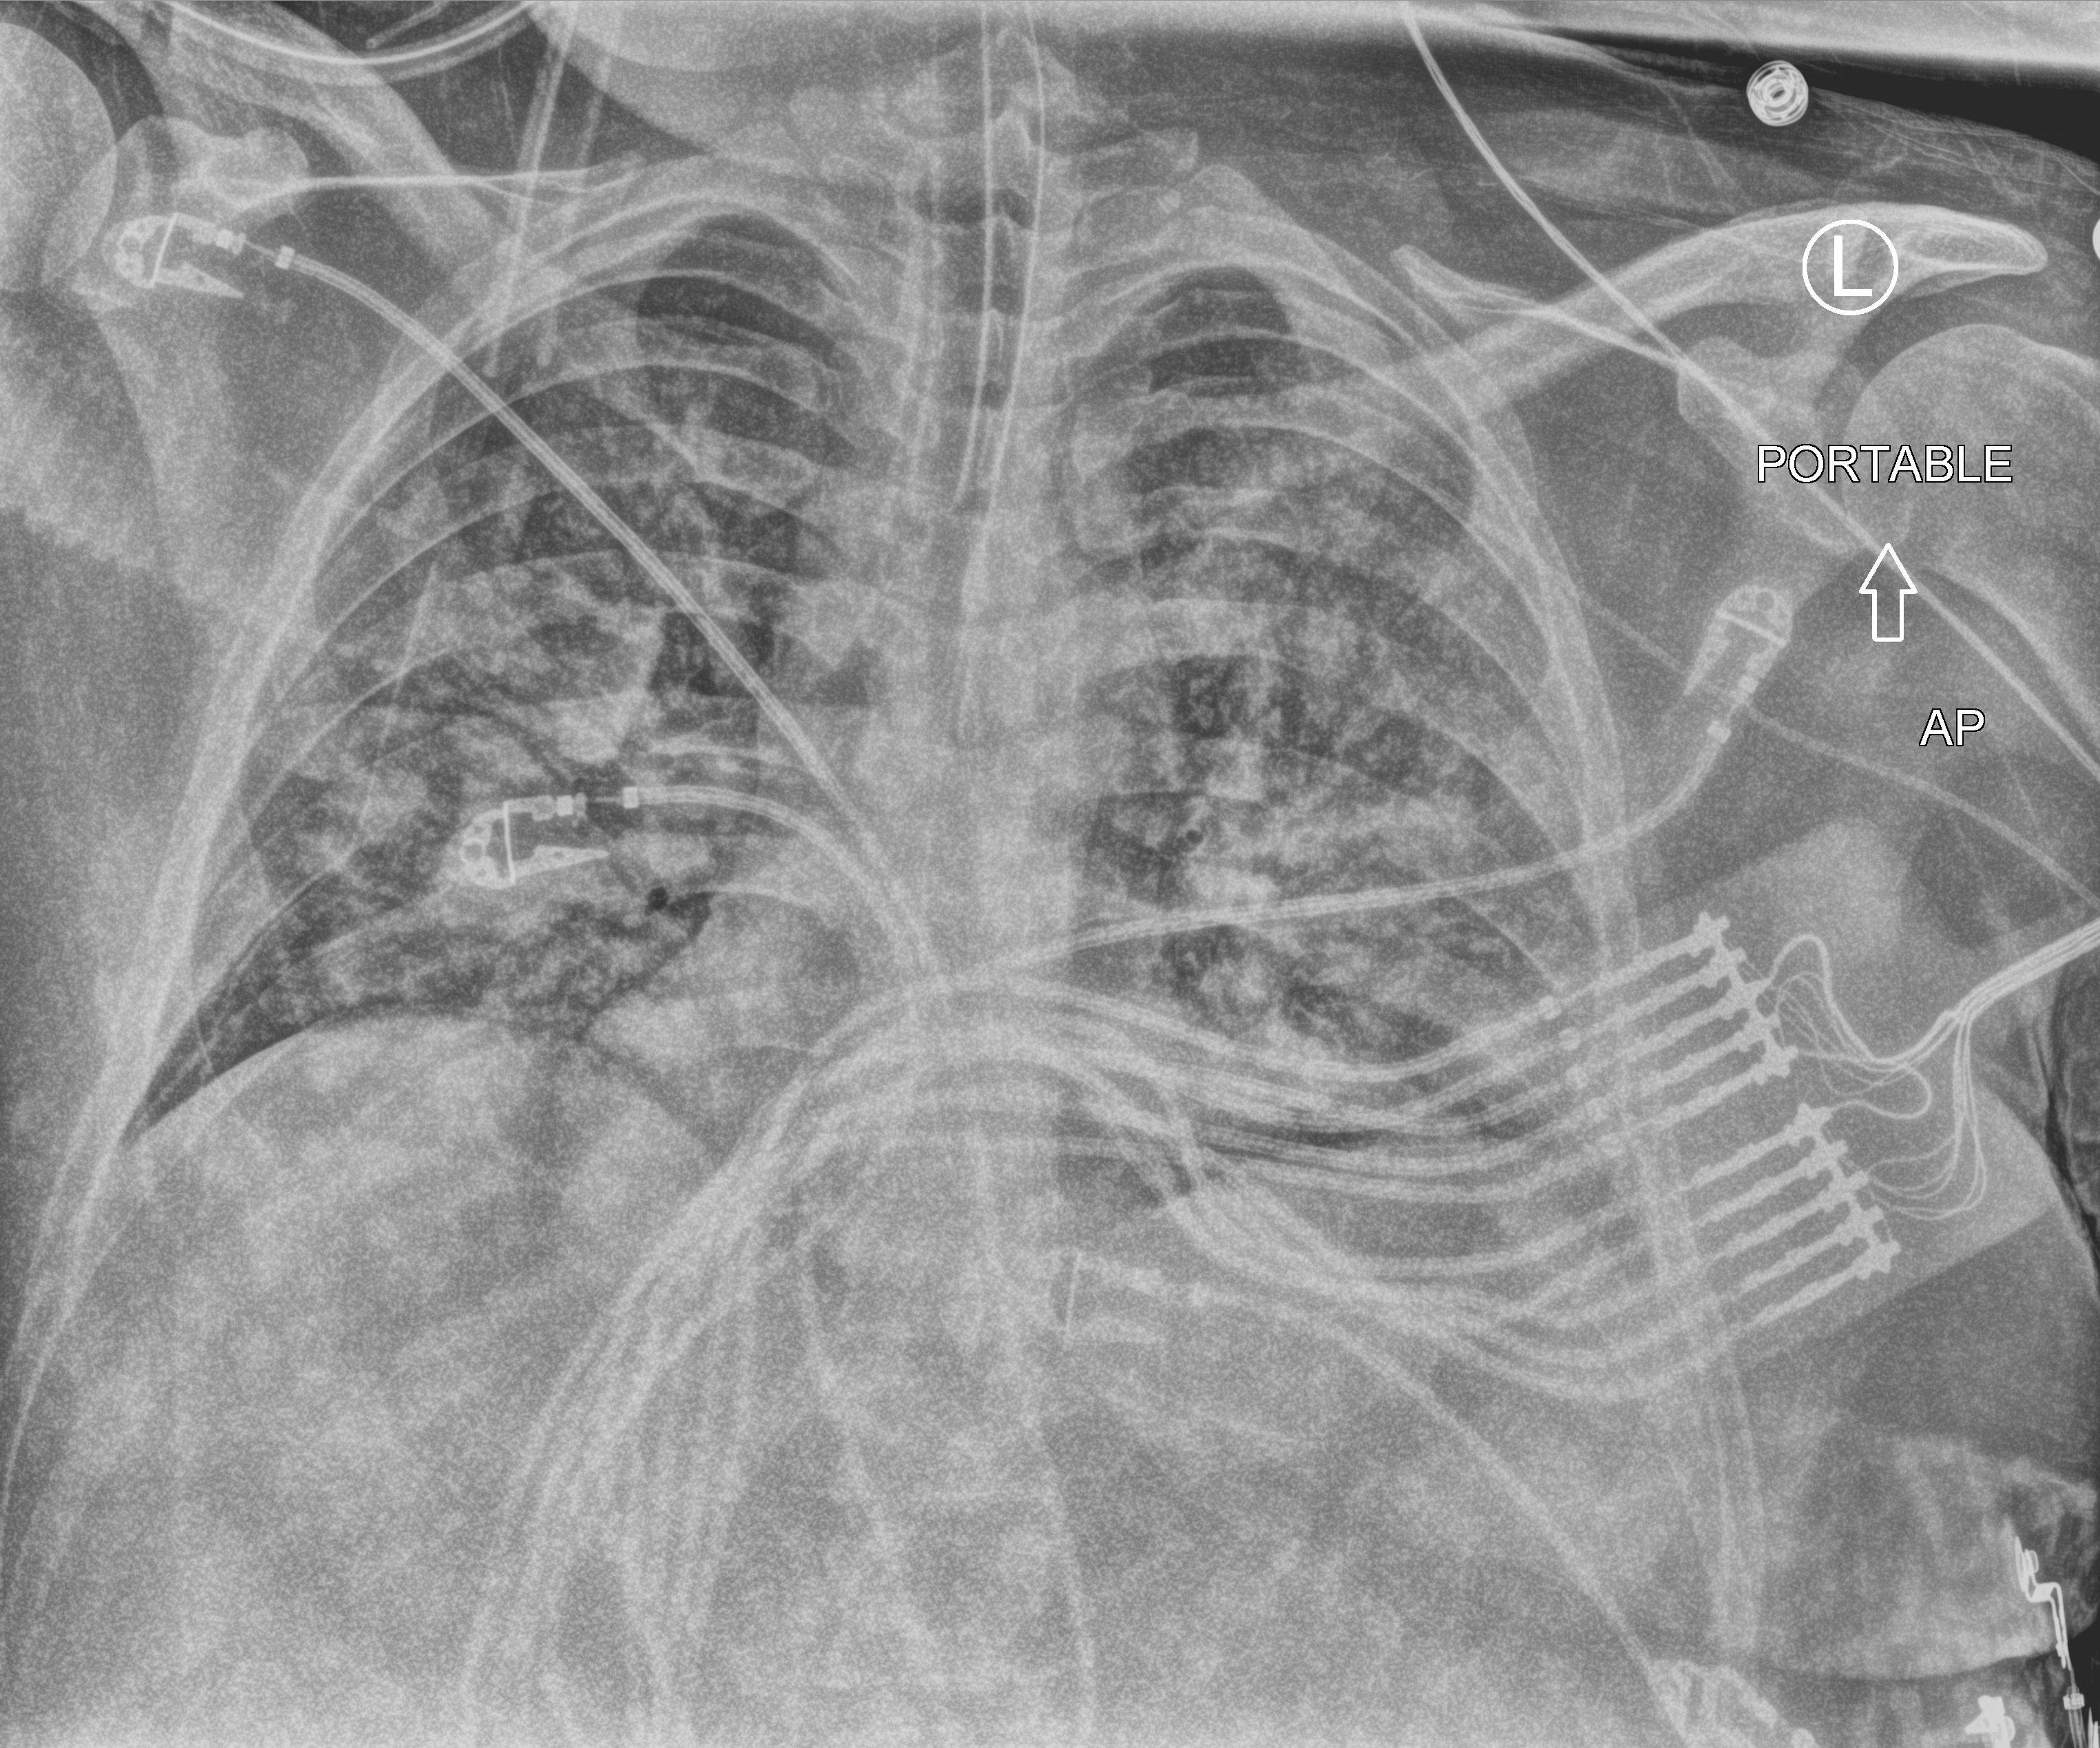
Portable chest radiograph. Adult patient hospitalised with COVID-19, age 18–59 years.
Hospital-stay facts (about this admission, not read from this image; timing relative to this image not recorded): admitted to intensive care during this hospital stay: yes.